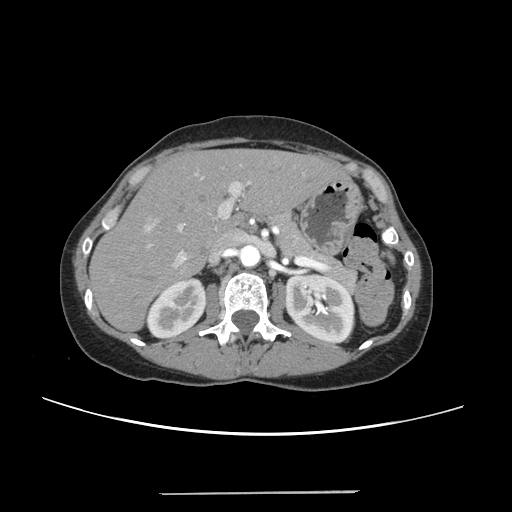
Contrast-enhanced abdominal CT, one axial slice; position 149 of 240 along the scan axis; 120 kVp; soft-tissue window (W 400 / L 40 HU); 1.25 mm slice thickness; 512 × 512 image matrix. Female patient, age 60 years. From the clinical record (not read from this slice): diagnosis: colorectal cancer liver metastases, imaged before liver resection.
Structures marked on this image (expert manual segmentation):
- liver: box from (x=92, y=150) to (x=344, y=329) px
- planned liver remnant (the part of the liver to remain after resection): (x=92, y=150)–(x=343, y=329)
- portal vein (with intrahepatic branches): (x=143, y=164)–(x=252, y=266)